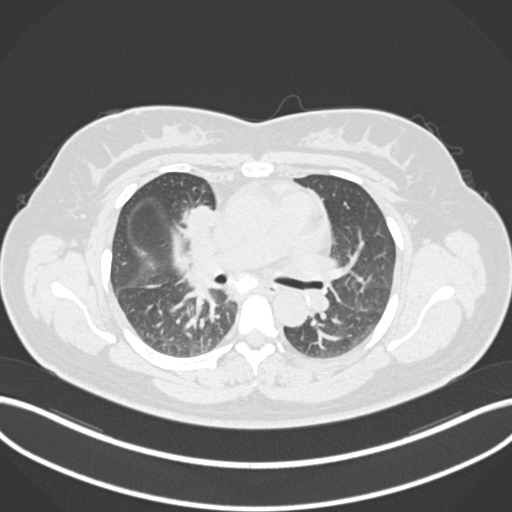
Chest CT, one axial slice; position 101 of 183 along the scan axis; 120 kVp; lung window (W 1500 / L -600 HU); 1 mm slice thickness; 512 × 512 image matrix, field of view 400 × 400 mm. Patient: female, 46 years. From the clinical record (not read from this slice): clinical TNM (as recorded): T2a N1 M0.
Outlined on this slice (bounding box drawn by a radiologist):
- lung tumour (recorded histology: adenocarcinoma): bounding box (x1, y1, x2, y2) in pixels: (179, 205, 222, 234)